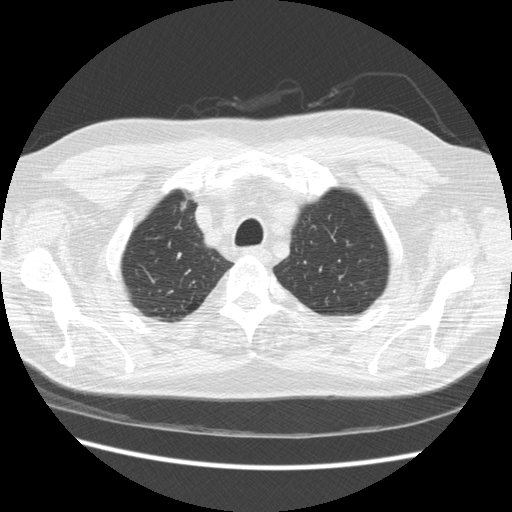
Low-dose screening chest CT, one axial slice. Slice 195 of 234 in the series (ordered by position). Reconstruction kernel STANDARD. Lung window (W 1500 / L -600 HU). 2.5 mm slice thickness. 512 × 512 image matrix, field of view 360 × 360 mm.
Outlined on this slice (manually delineated by an expert):
- lesion 1 (tumor, upper lobe of right lung): bounding box (x1, y1, x2, y2) in pixels: (181, 200, 187, 210)